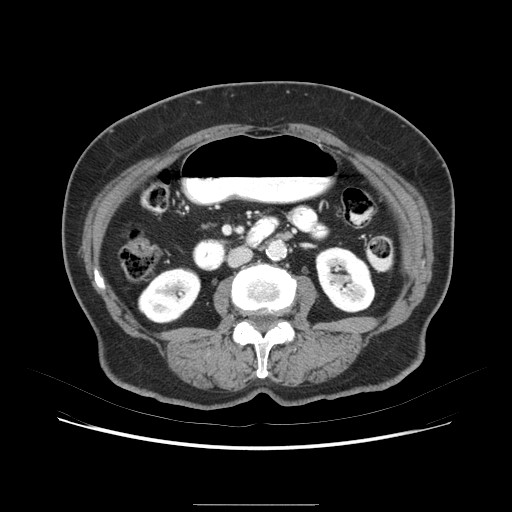
Contrast-enhanced abdominal CT (liver protocol), one axial slice. 120 kVp. Soft-tissue window (W 400 / L 40 HU). 2.5 mm slice thickness. 512 × 512 image matrix. From the clinical record (not read from this slice): diagnosis: hepatocellular carcinoma (patient treated with transarterial chemoembolisation; whether this scan precedes or follows treatment is not stated here); TNM stage (as recorded): Stage-I; Child-Pugh class: A; tumour differentiation: poorly differentiated; tumour nodularity: uninodular.
Outlined on this slice (semi-automatically segmented with operator editing):
- liver parenchyma outside the tumour (the mass and vessels are separate outlines, so this box may not span the whole liver): box from (x=106, y=225) to (x=112, y=238) px